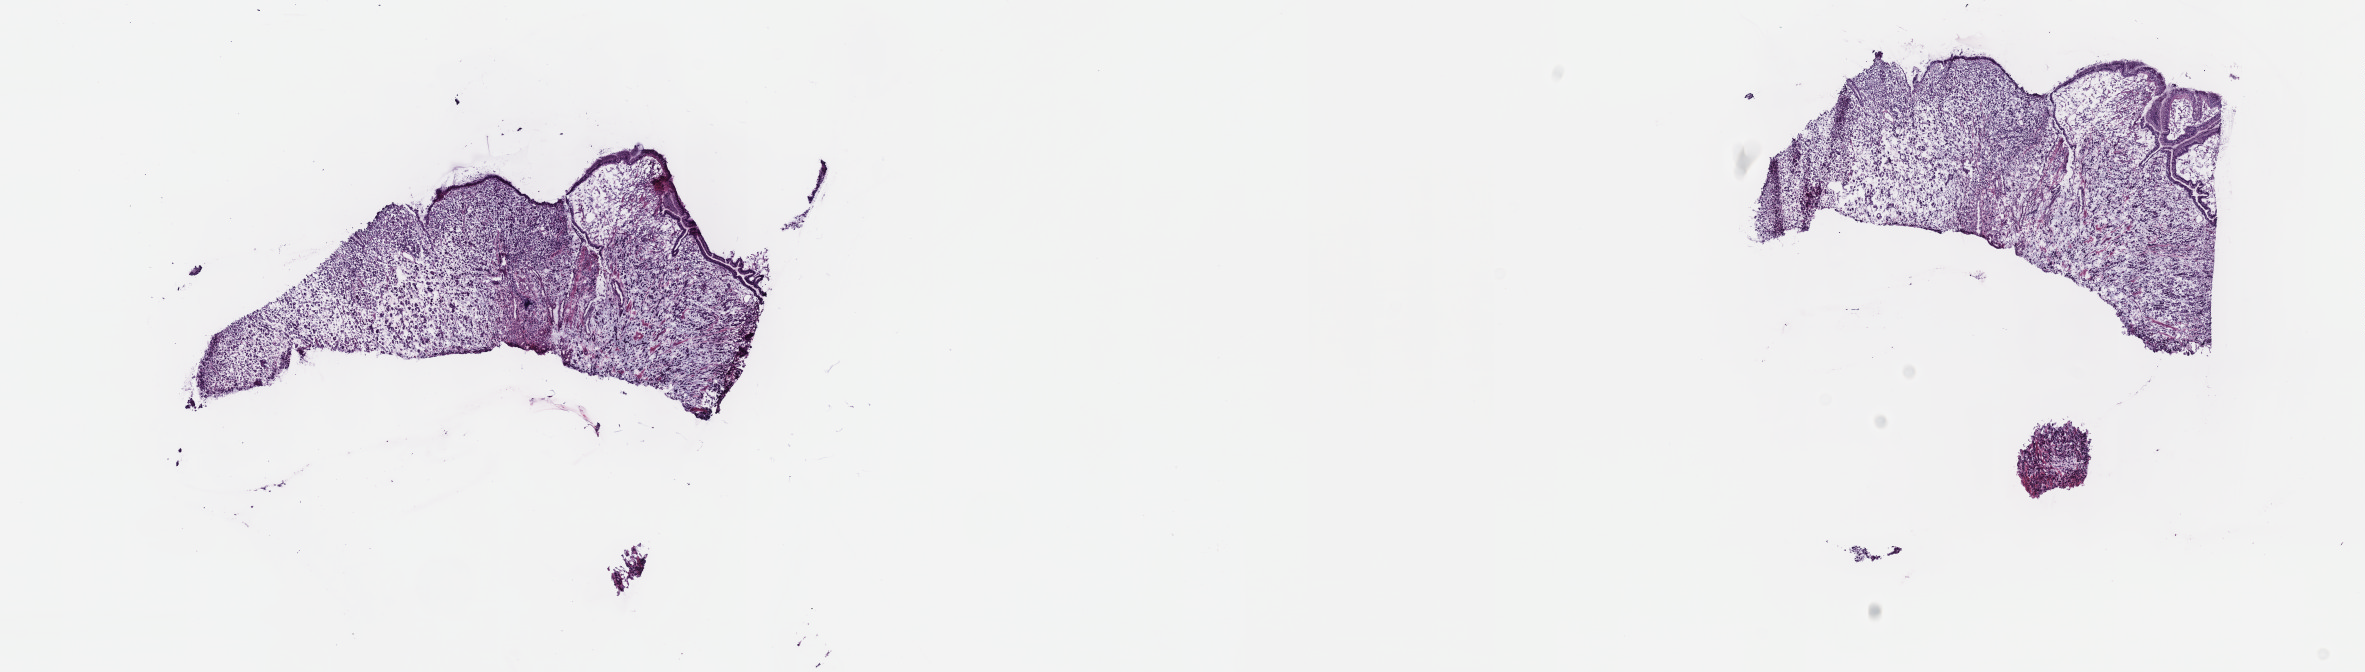
Digitized H&E-stained tissue section (whole slide), a low-resolution overview of the entire scanned area, about 19.1 x 5.4 mm. Frozen section from the top of the tissue portion. Primary tumour sample from the stomach. Male patient; age at initial diagnosis 65 years. Slide review estimates, as recorded: tumour cells 85%, tumour nuclei 90%.
Histologic diagnosis: Signet ring cell carcinoma (gastric antrum).